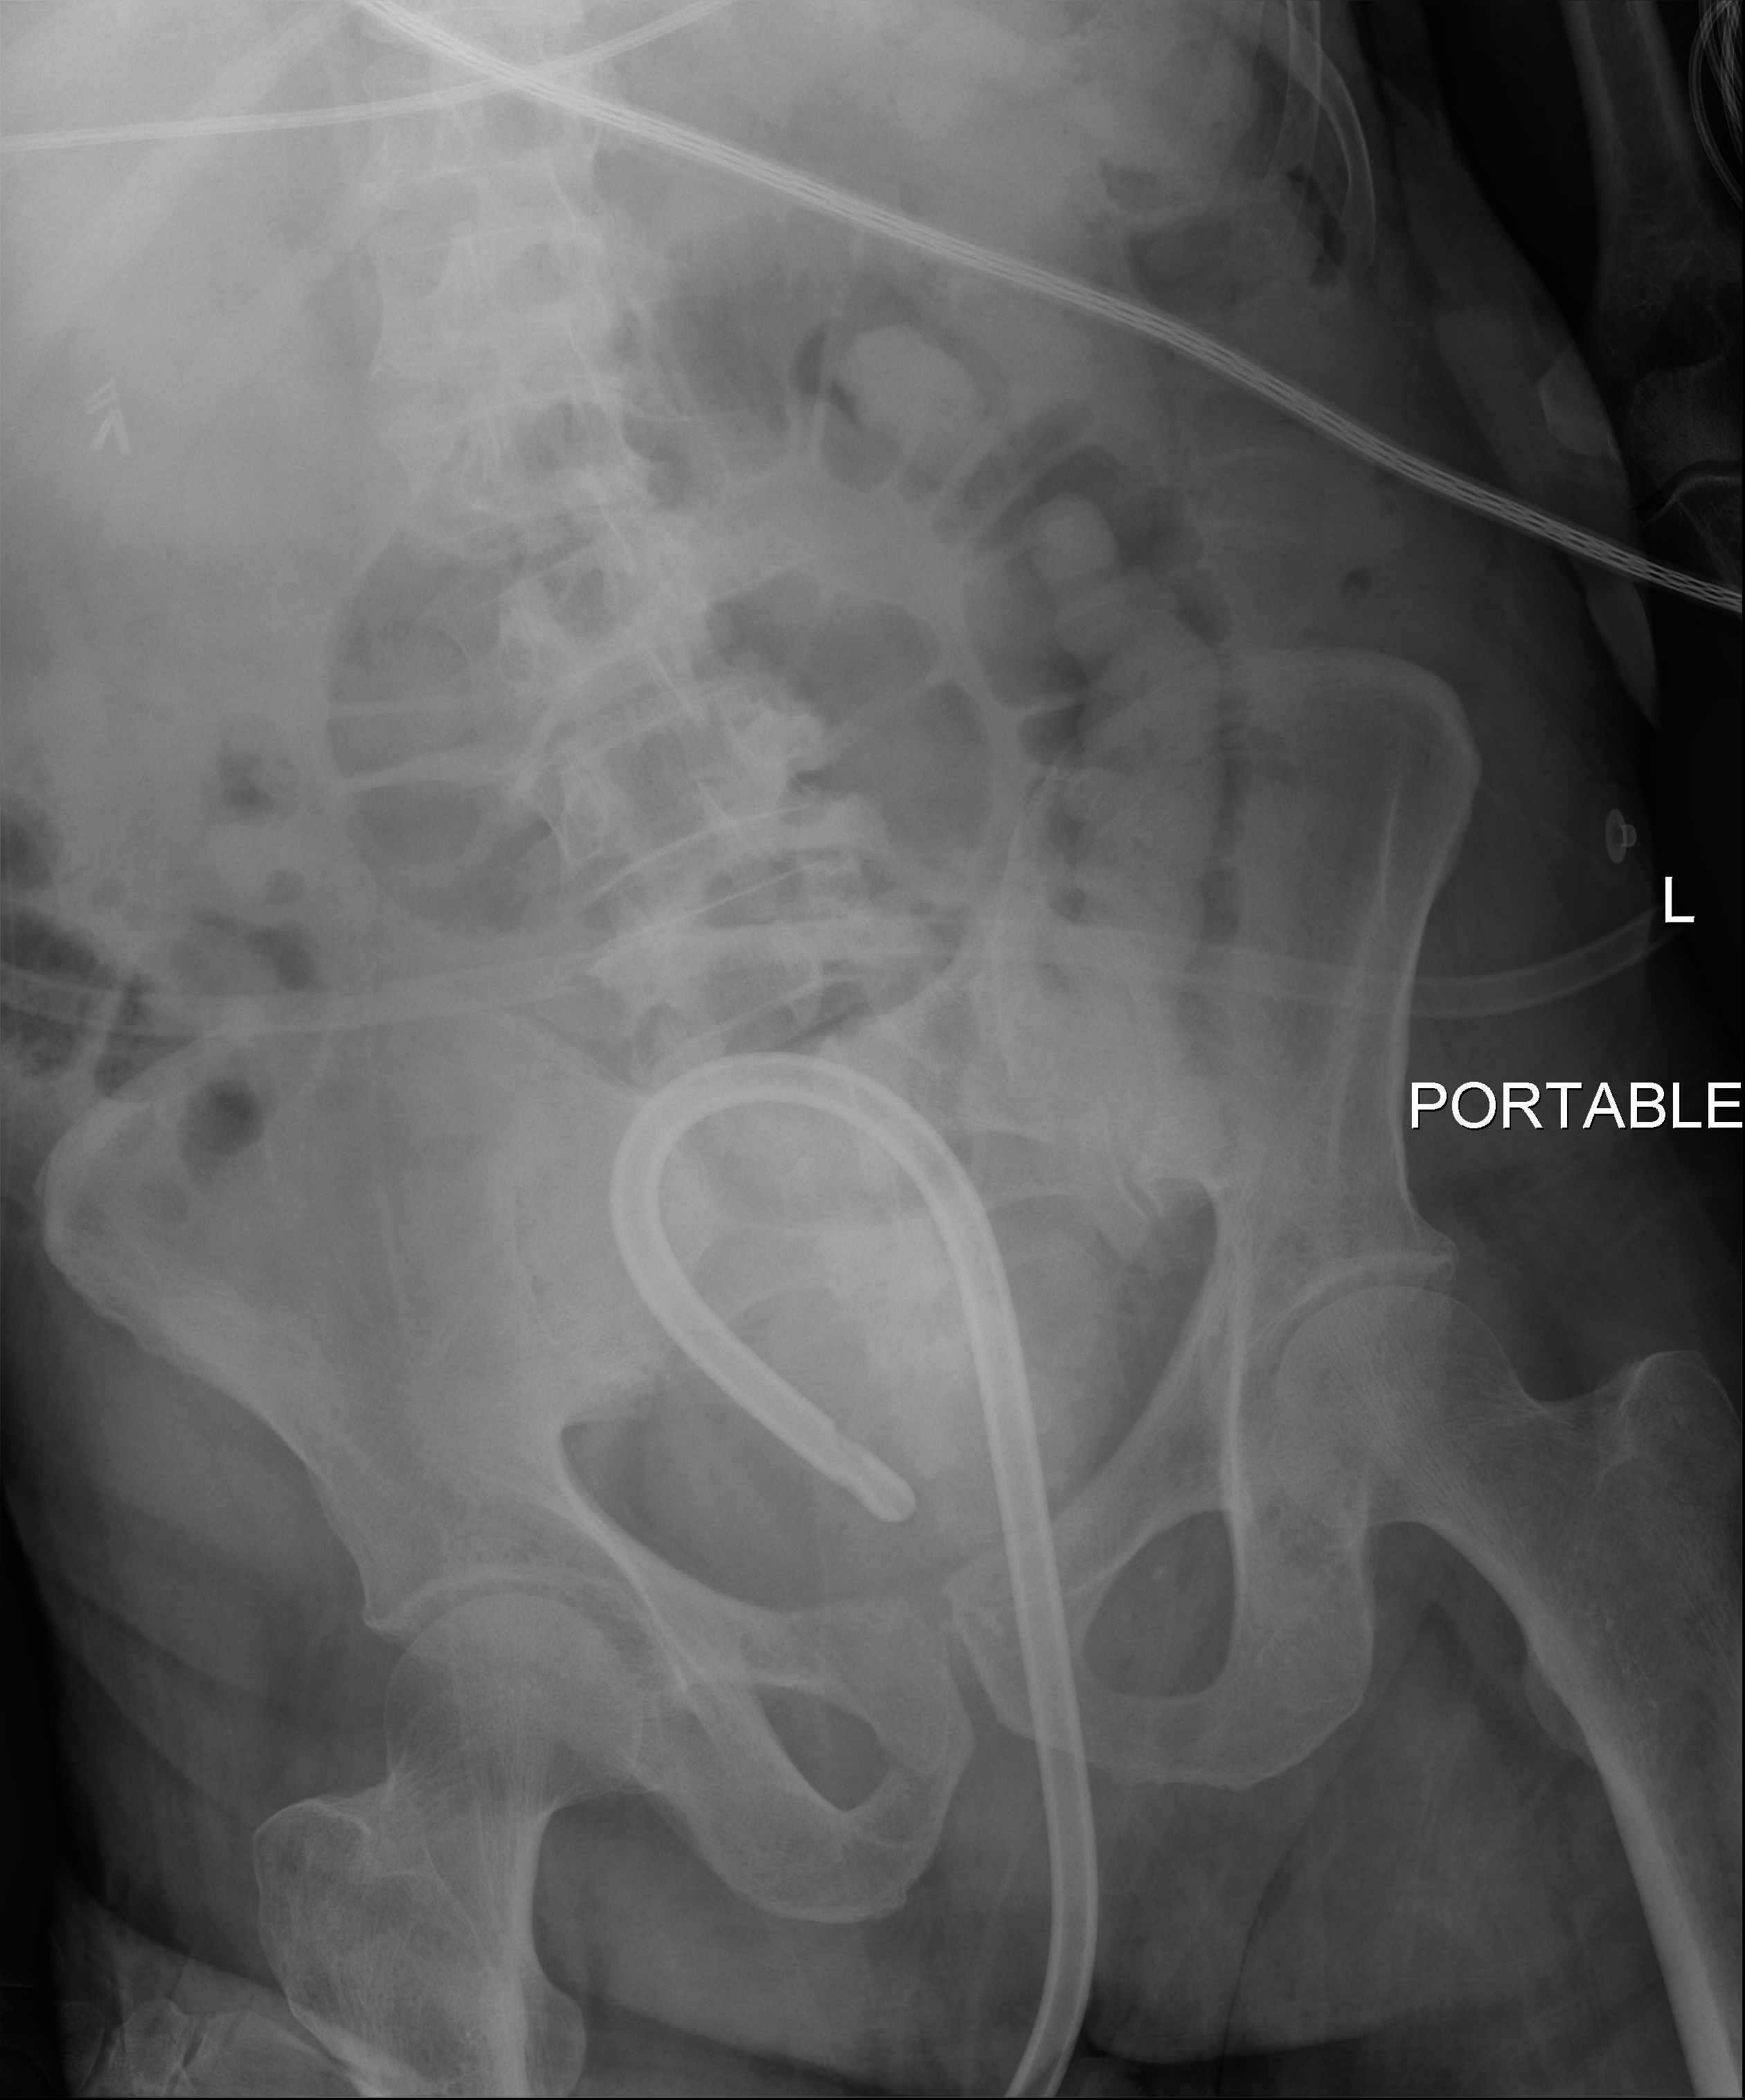
Abdomen radiograph (digital radiography); anteroposterior (AP) projection. Patient hospitalised with COVID-19; male, aged 75–90 years.
From the hospital-stay record, not from the radiograph (when in the stay this image was taken is not recorded):
- diabetes (admission record): no